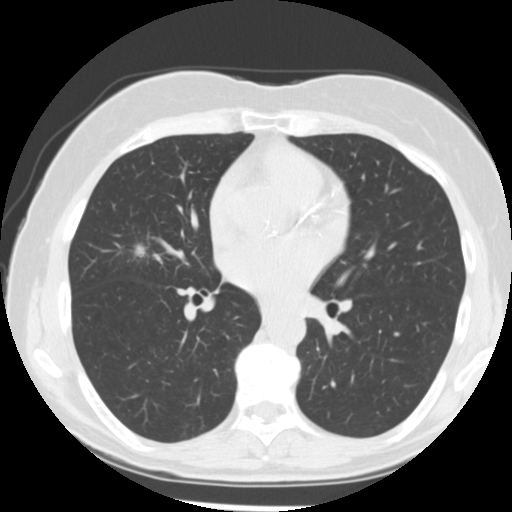
Low-dose screening chest CT, axial slice. Baseline annual screen. Lung window (W 1500 / L -600 HU). Standard (soft-tissue) reconstruction kernel (STANDARD). 512 × 512 image matrix, field of view 320 × 320 mm. Female participant, aged 66 years at enrolment.
• Expert-annotated lung lesion, box from (x=126, y=240) to (x=161, y=271) px.
• The exam's reader record, not a measurement of the box and not confirmed to be the same lesion: non-calcified nodule or mass ≥4 mm, right middle lobe, 15 × 13 mm, poorly defined margins, soft tissue attenuation.